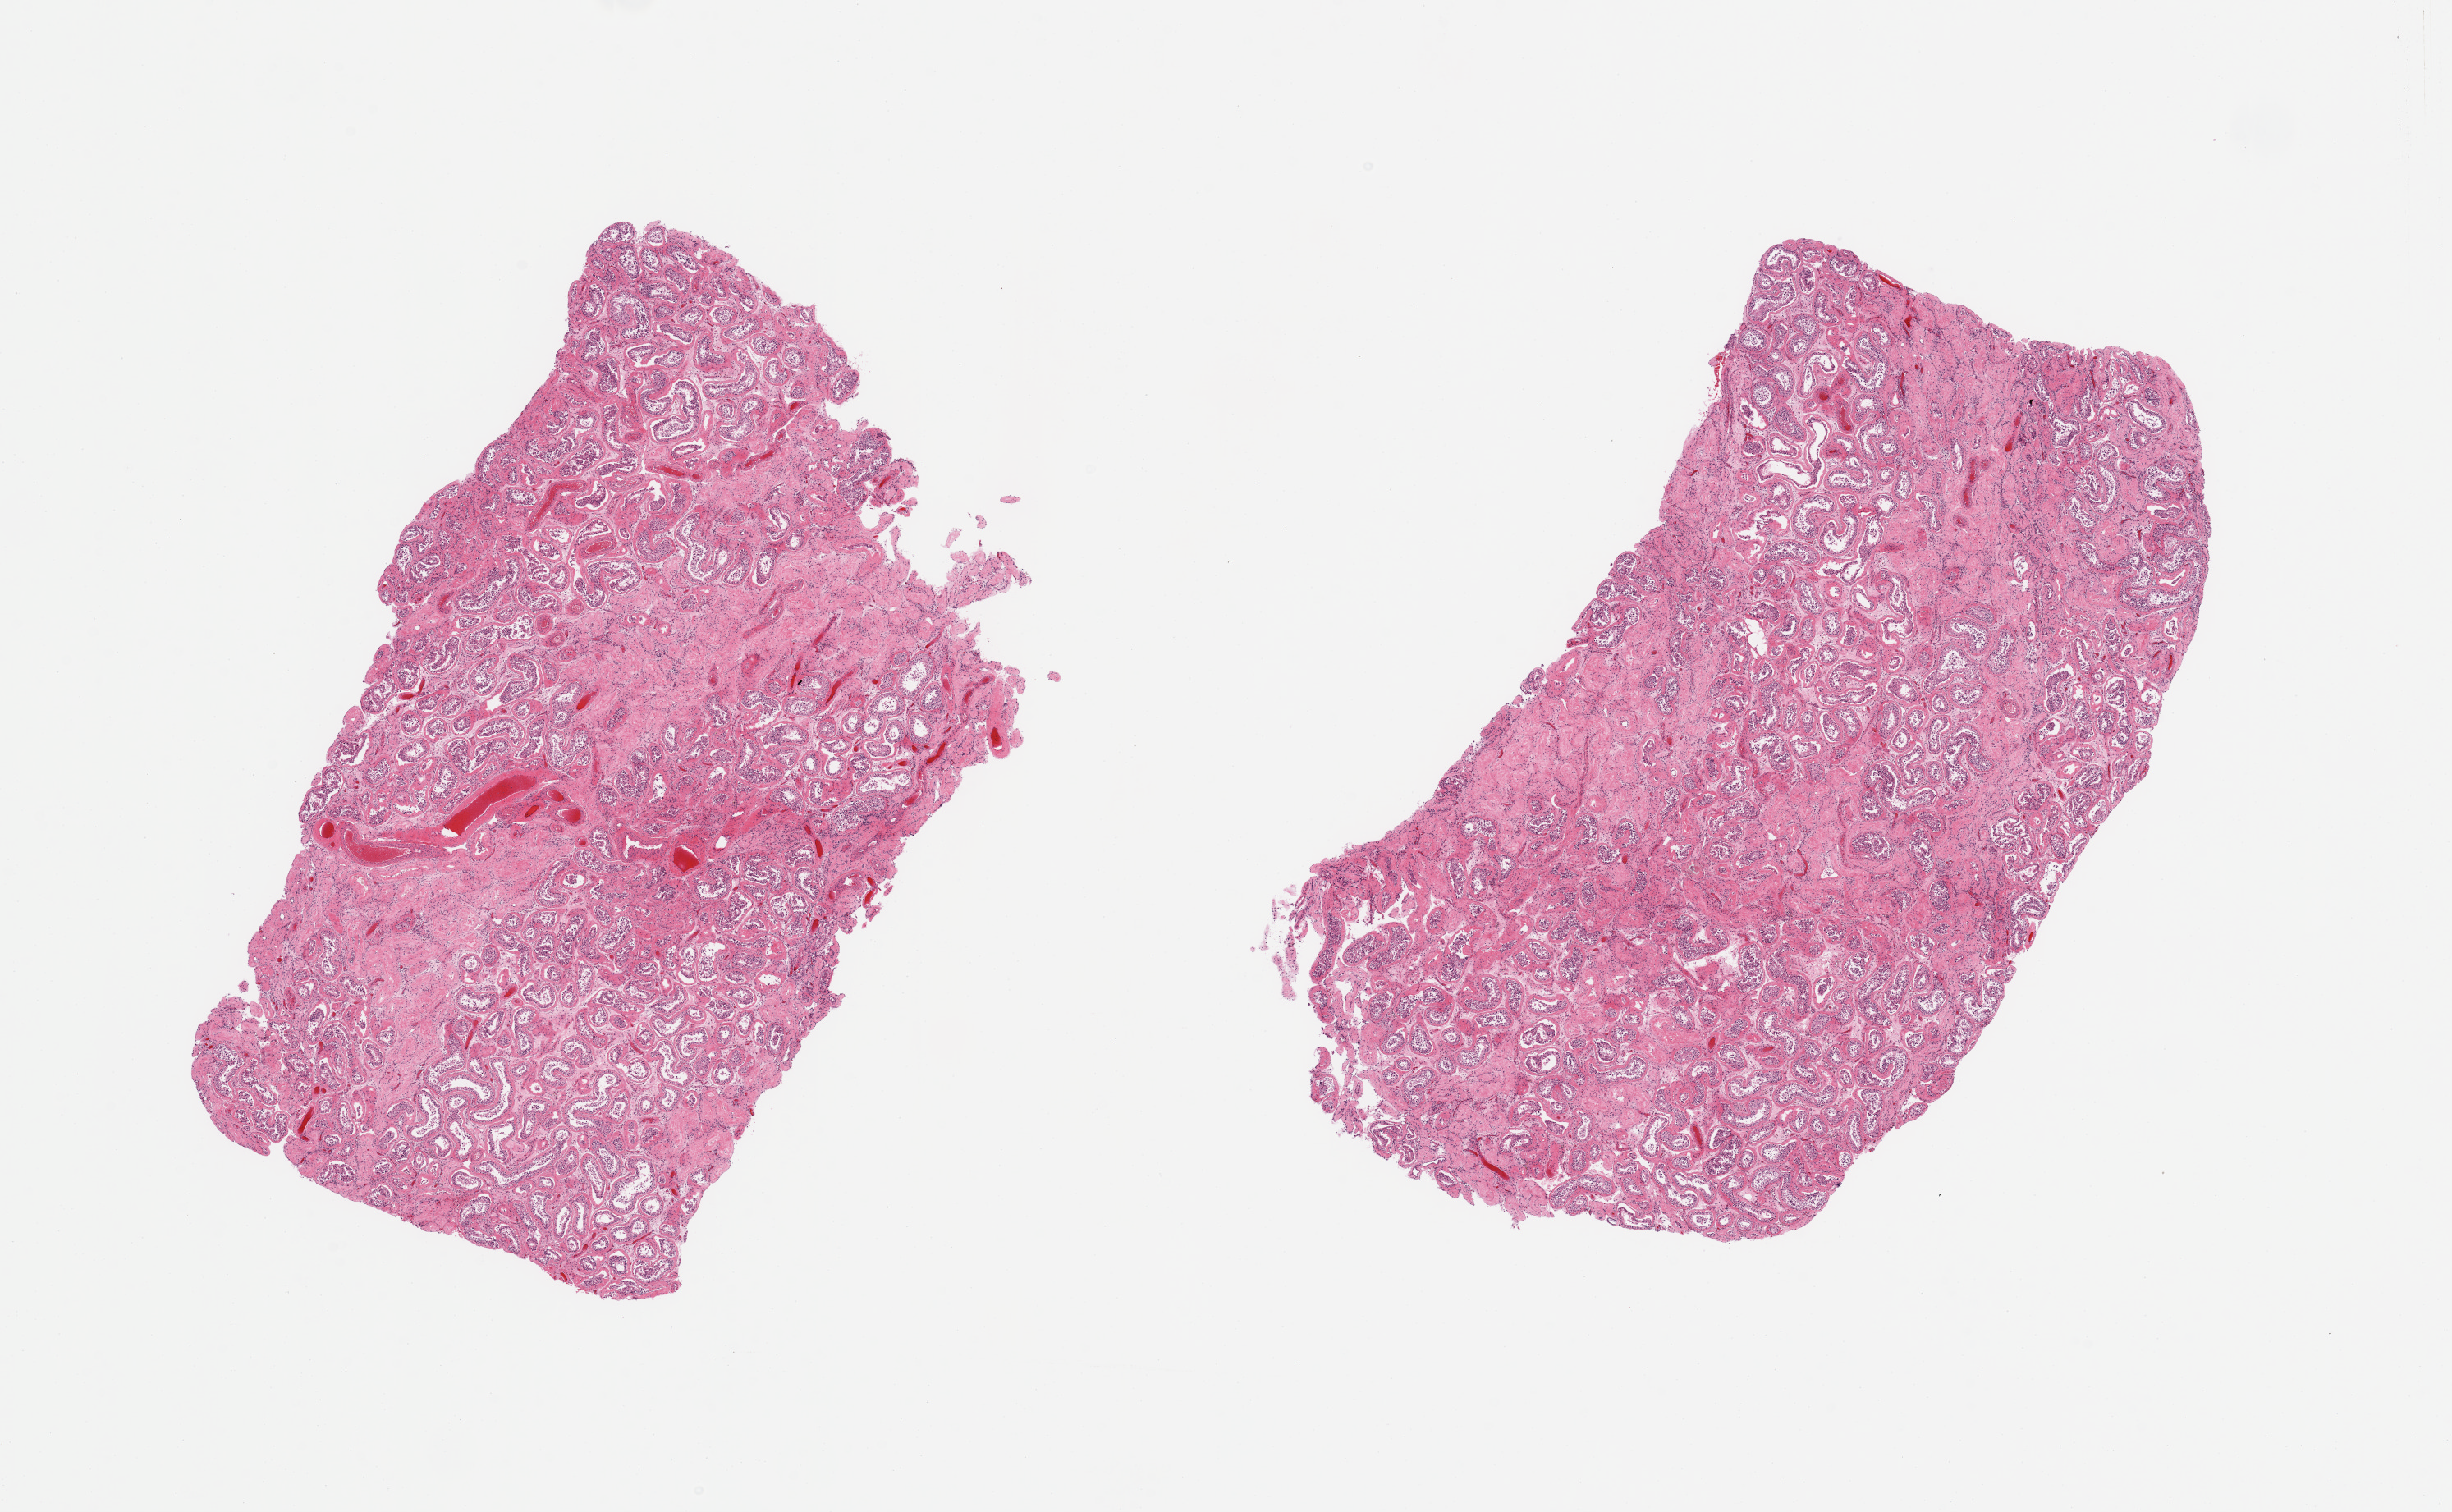
Digitized H&E-stained section, low-resolution overview of the scanned area, about 23.6 x 14.6 mm; PAXgene-fixed paraffin-embedded (PFPE) section; section of testis (target tissue); donor tissue sample. Donor: male.
Review note (as recorded): 2 pieces; spermatogenesis greatly reduced; 30% parenchymal fibrosis.